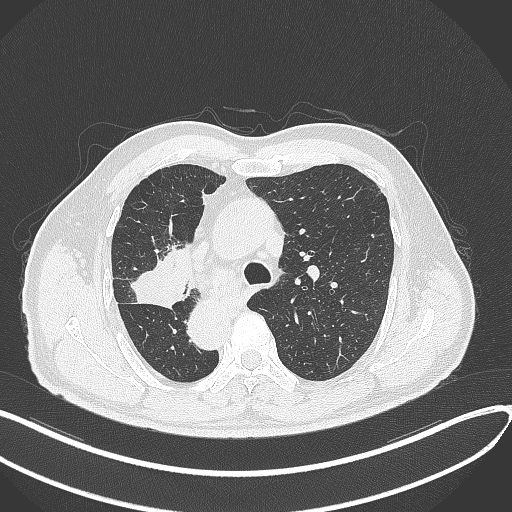
Chest CT, one axial slice. Position 213 of 300 along the scan axis. Reconstruction kernel B70f. Lung window (W 1500 / L -600 HU). 512 × 512 image matrix, field of view 400 × 400 mm. Patient: male, 67 years. From the clinical record (not read from this slice): clinical TNM (as recorded): T2a N0 M0.
Annotated regions visible in this slice (bounding box drawn by a radiologist):
- lung tumour (recorded histology: squamous cell carcinoma): bounding box <125,254,191,308> (left, top, right, bottom; pixels)